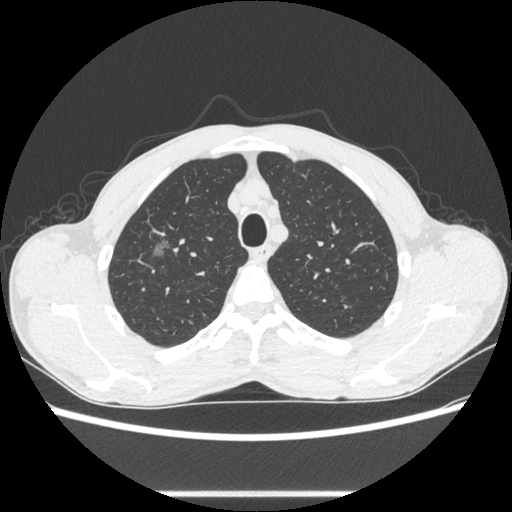
Chest CT, one axial slice; position 477 of 600 along the scan axis; reconstruction kernel STANDARD; 100 kVp; lung window (W 1500 / L -600 HU); 0.62 mm slice thickness; 512 × 512 image matrix, field of view 357 × 357 mm. Patient: male, 54 years. From the clinical record (not read from this slice): clinical TNM (as recorded): T1a N0 M0.
Outlined on this slice (bounding box drawn by a radiologist):
- lung tumour (recorded histology: adenocarcinoma): bounding box [x1, y1, x2, y2] px = [145, 235, 175, 264]